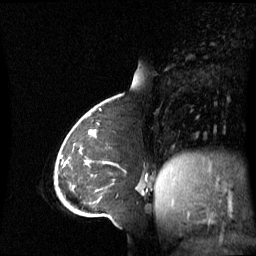
Breast MRI (dynamic contrast-enhanced), one sagittal slice. Position 20 of 60 along the scan axis. Dynamic contrast-enhanced series, image 2 of 3 at this slice position (ordered by acquisition). 1.5 T. TE 4.2 ms, TR 8.4 ms. 2.8 mm slice thickness. 256 × 256 image matrix, field of view 270 × 270 mm. Patient: female, 43 years. Case-level facts recorded for this patient, not image findings: setting: breast cancer imaged before/during neoadjuvant chemotherapy; receptor status: triple-negative.
Outlined on this slice (semi-automatic segmentation, software-assisted and operator-edited):
- analysis volume of interest (the breast-tissue region the enhancement analysis was run in; not a lesion): bounding box <69,137,143,198> (left, top, right, bottom; pixels)
- tumour enhancement mask (voxels above the 70 % enhancement threshold inside the analysis volume of interest): <107,162,110,164>